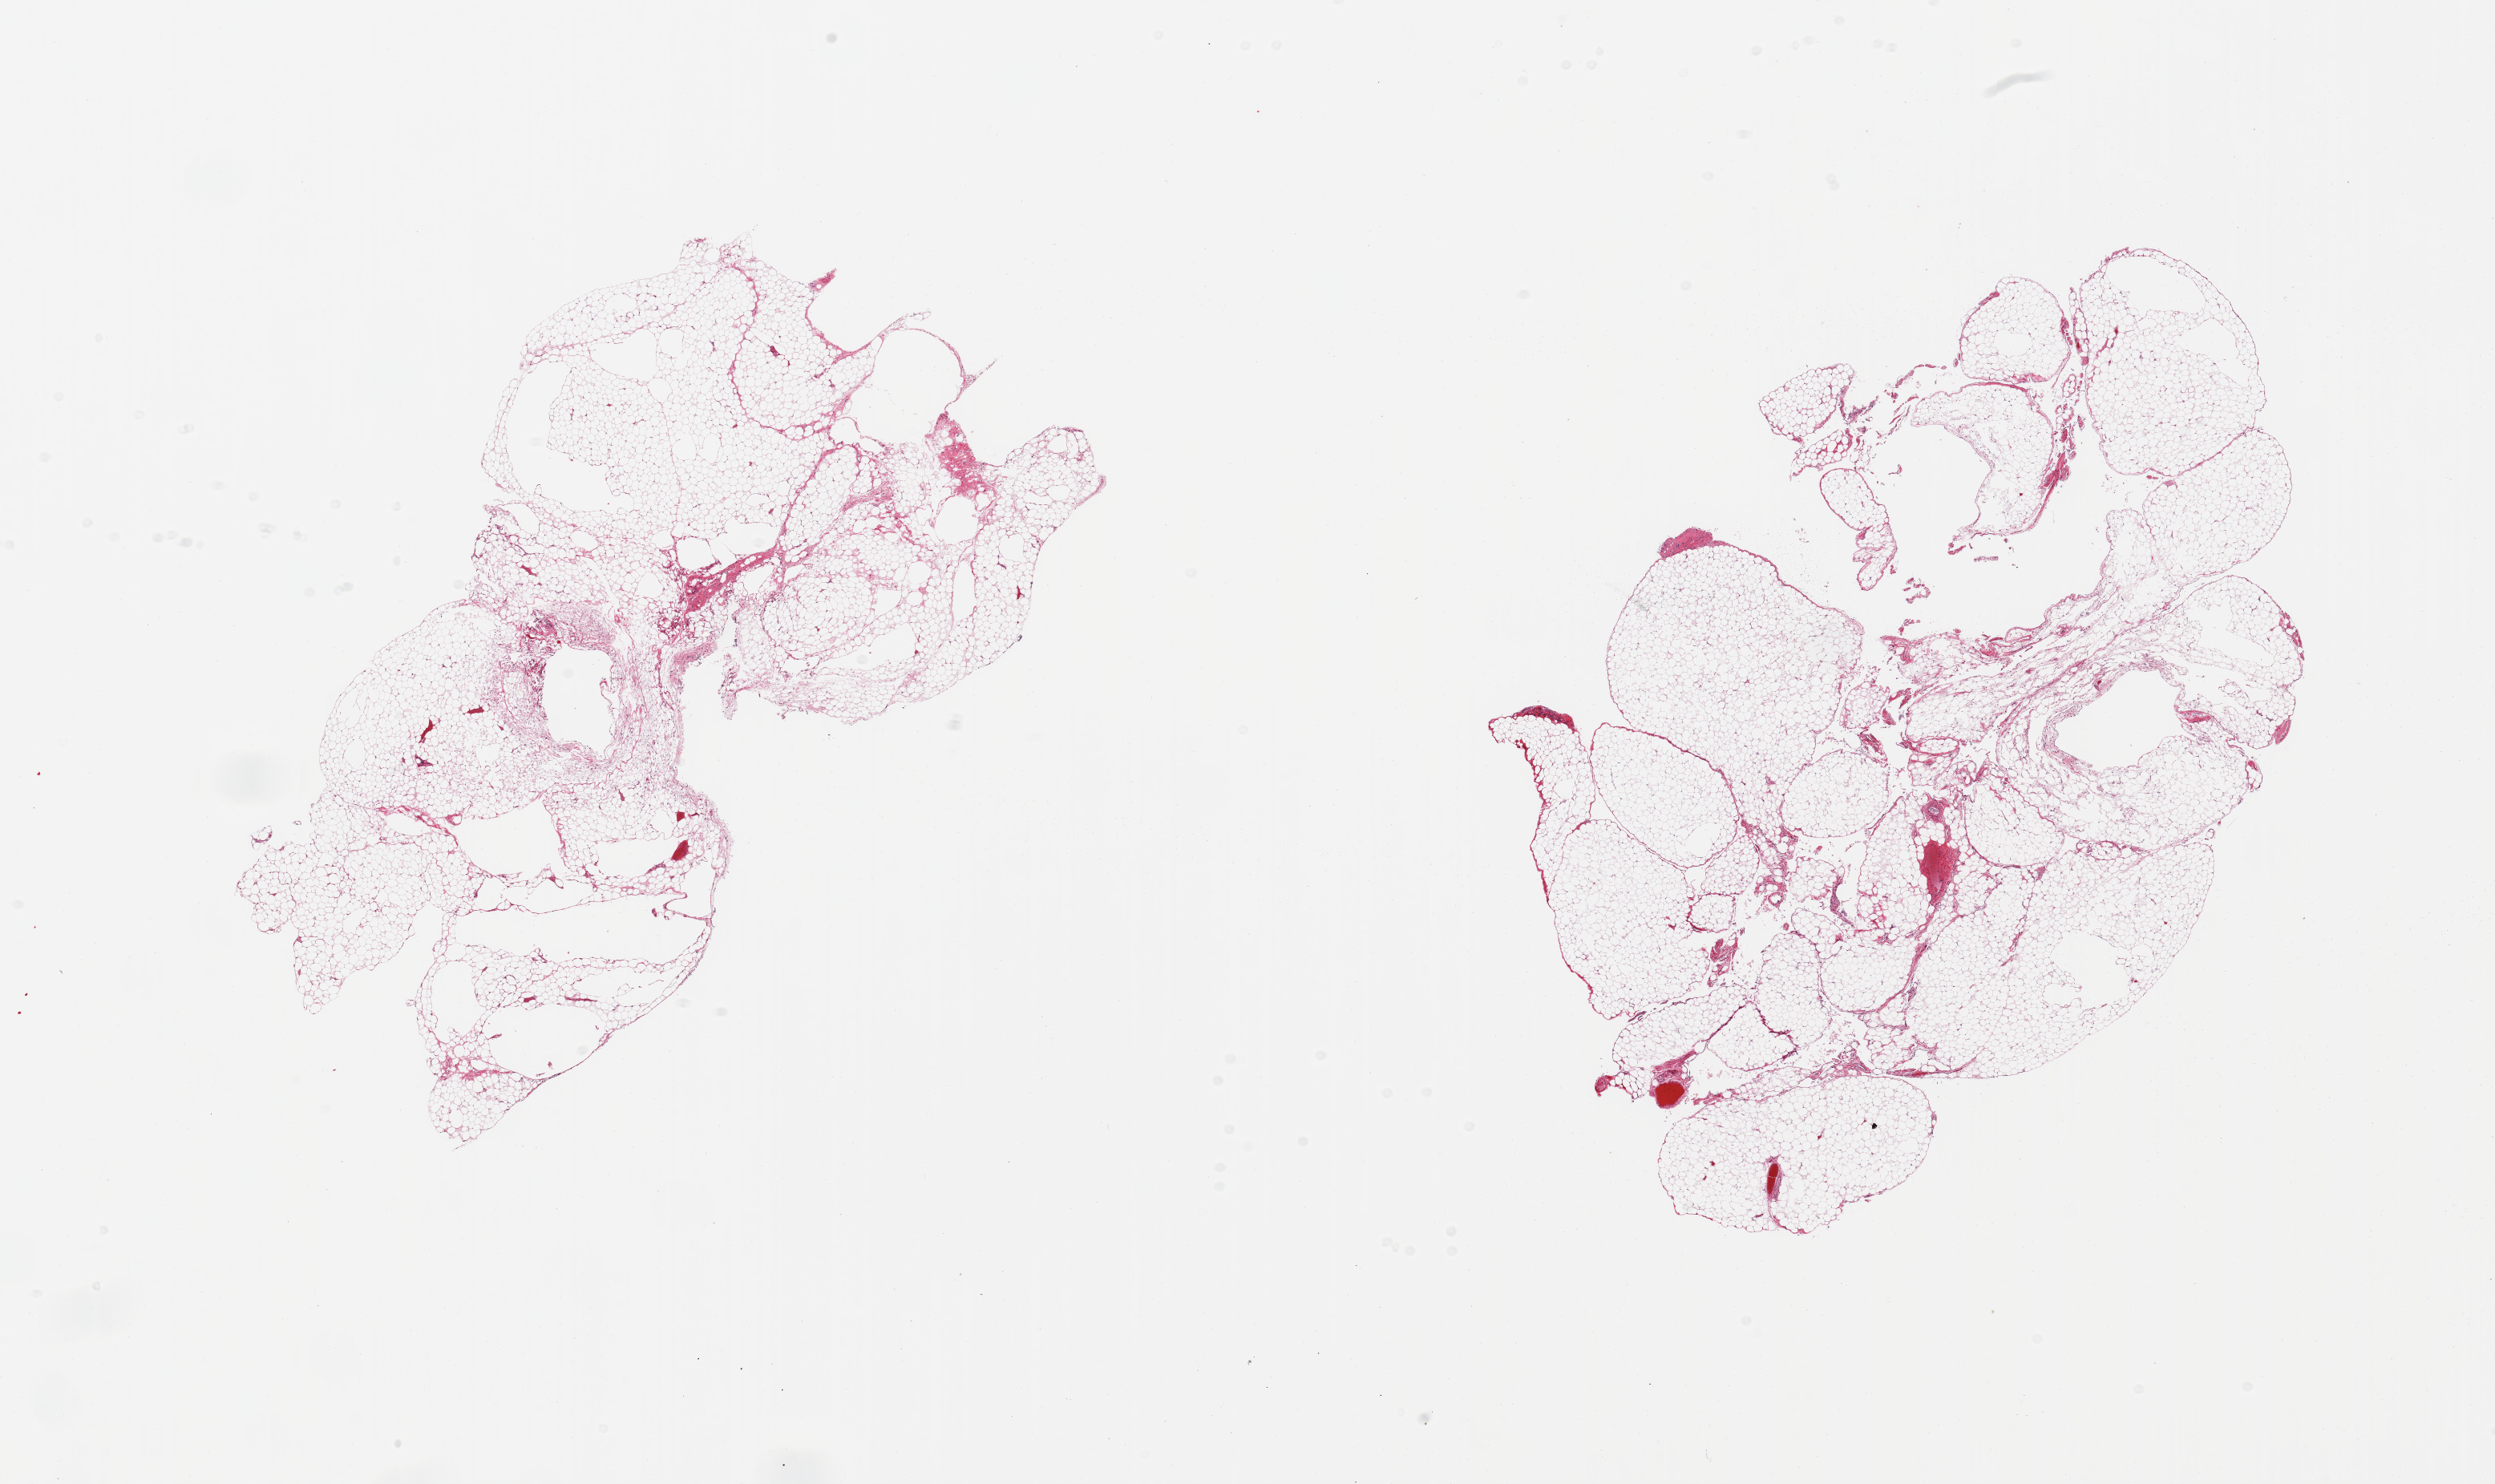
Digitized haematoxylin and eosin-stained section, brightfield — a low-resolution overview of the entire scanned area, about 24.6 x 14.6 mm (from a 20x scan); PAXgene-fixed, paraffin-embedded tissue; target tissue: omentum; donor tissue sample. Donor: female.
Pathologist's review note for this sample: 2 pieces, ~5-10% fascia/vascular elements.